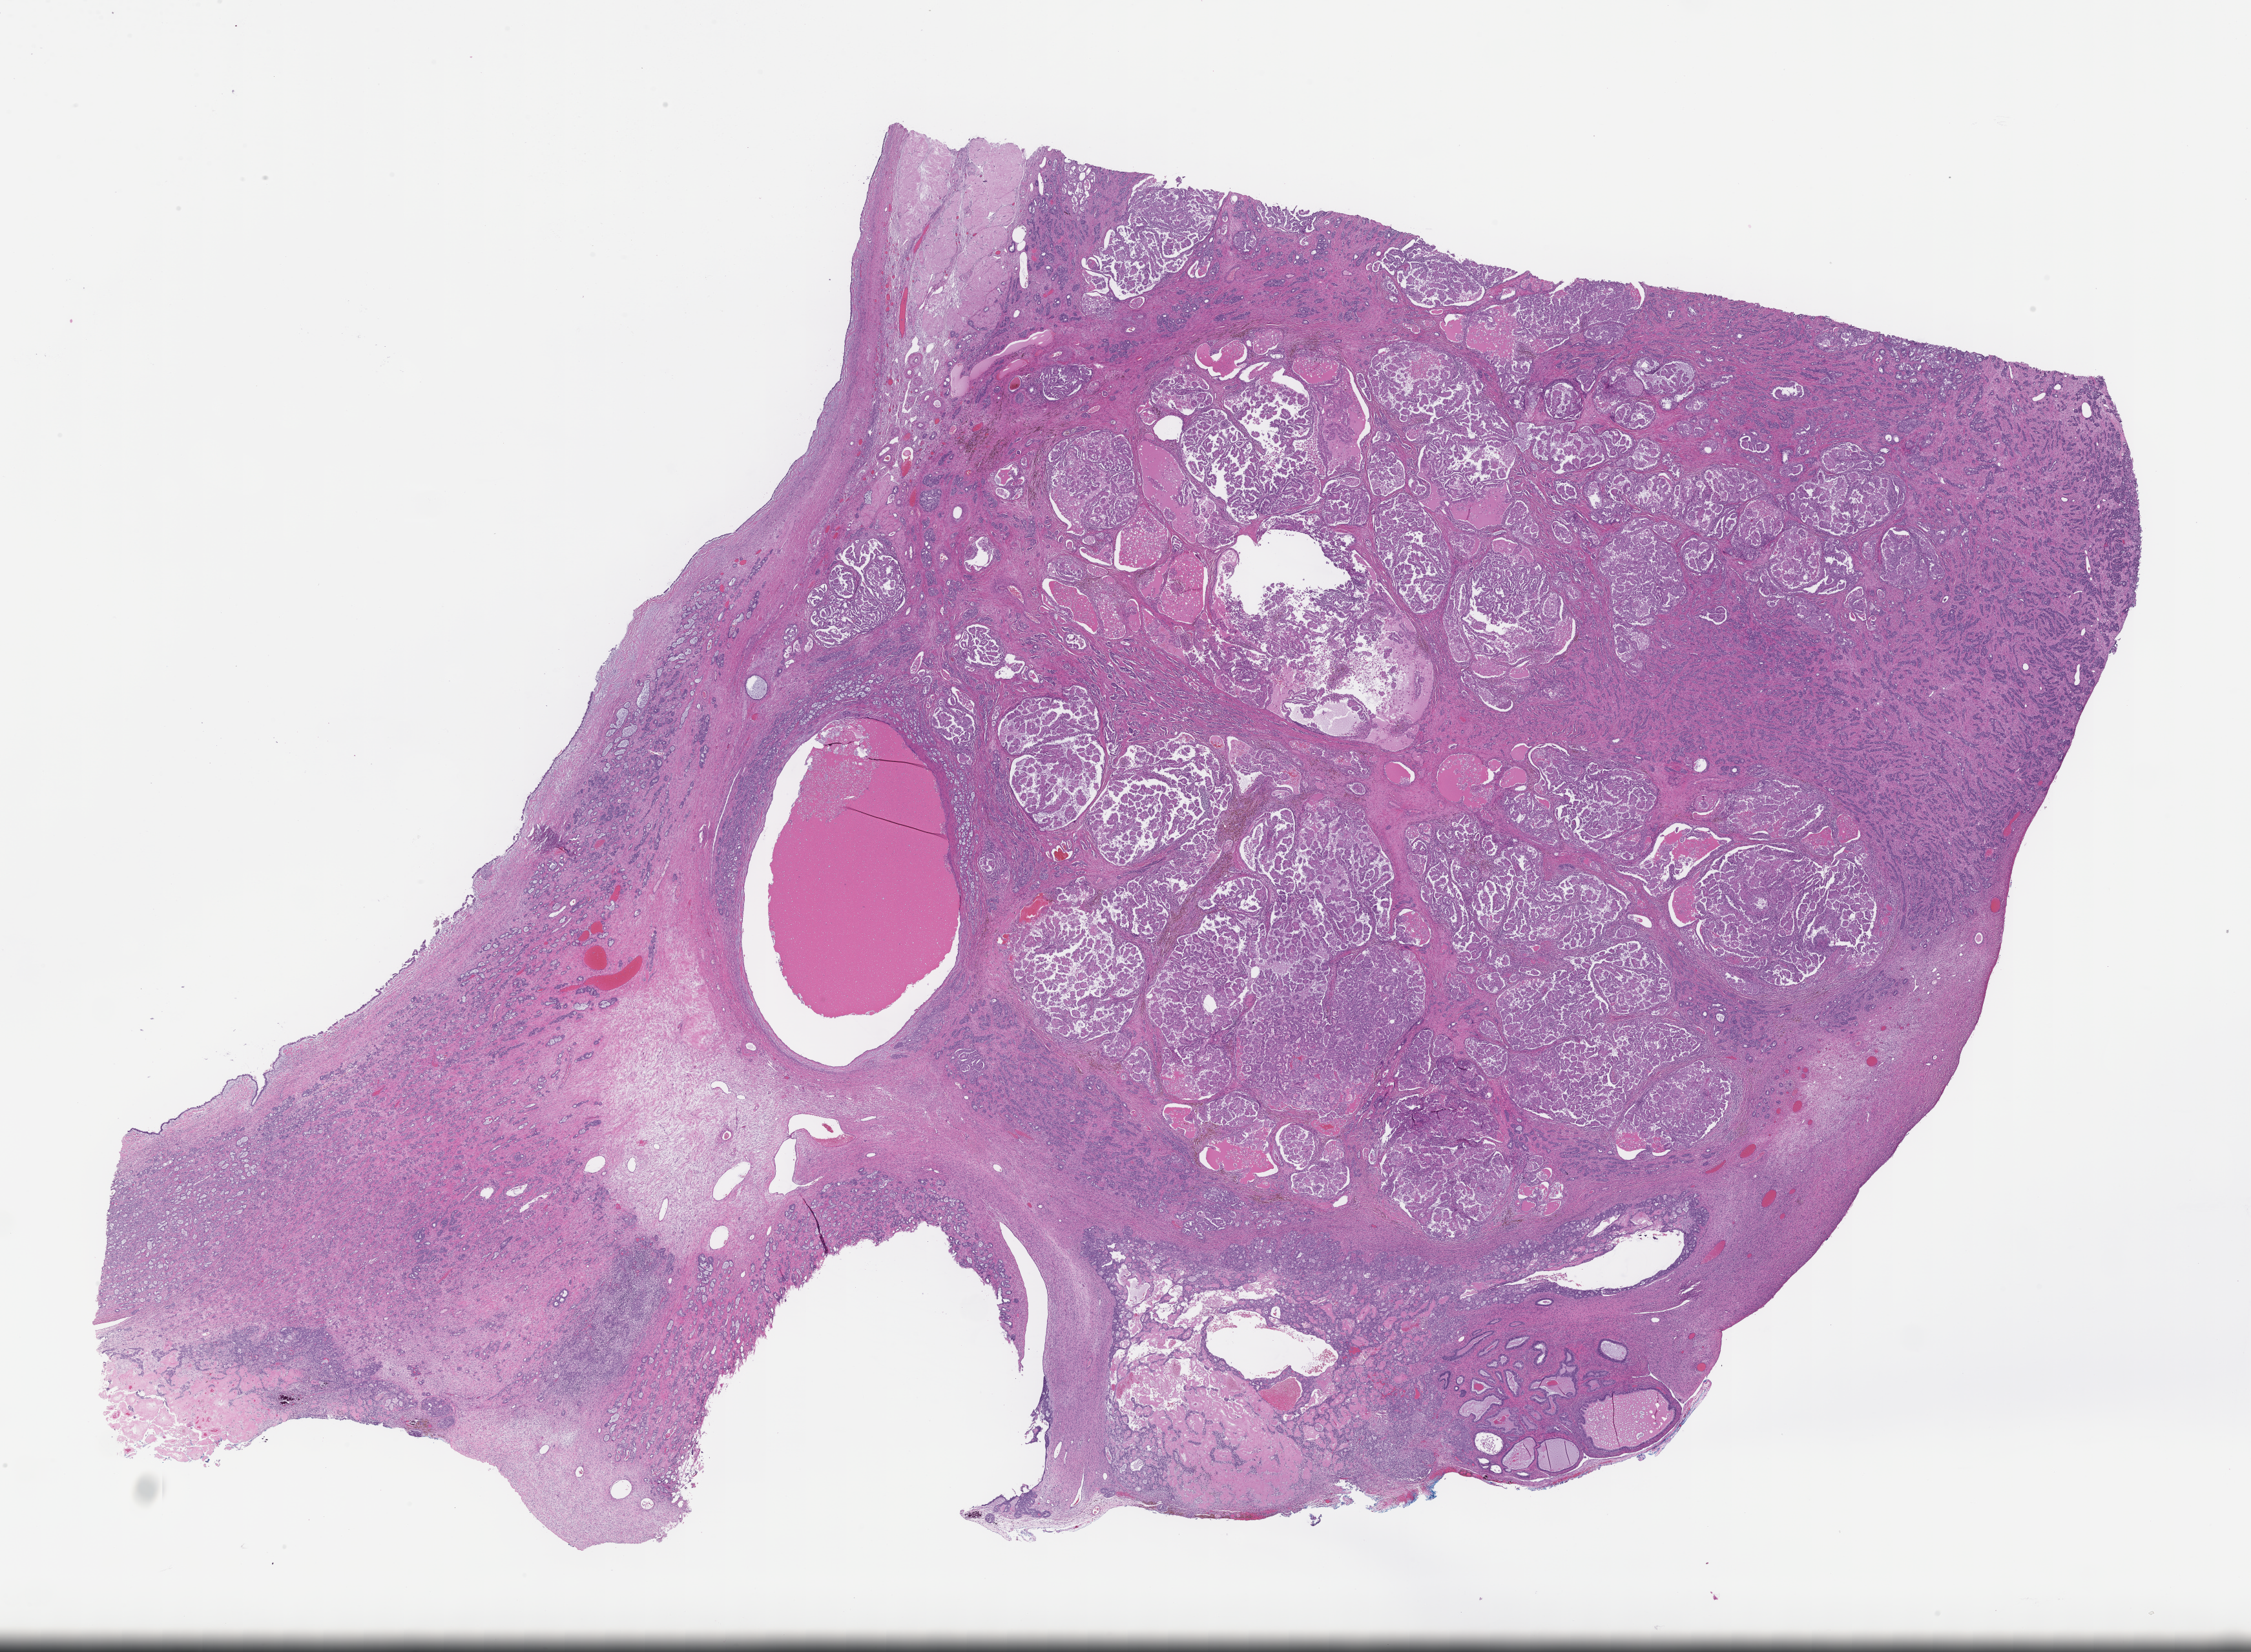
Hematoxylin and eosin (H&E) whole-slide image — a low-resolution overview of the entire scanned area, about 28.1 x 20.7 mm. FFPE section. Tissue site: ovary. Specimen time point: archival tissue. Patient sex: female.
- this section: primary tumour tissue
- diagnosis: Ovarian Carcinoma